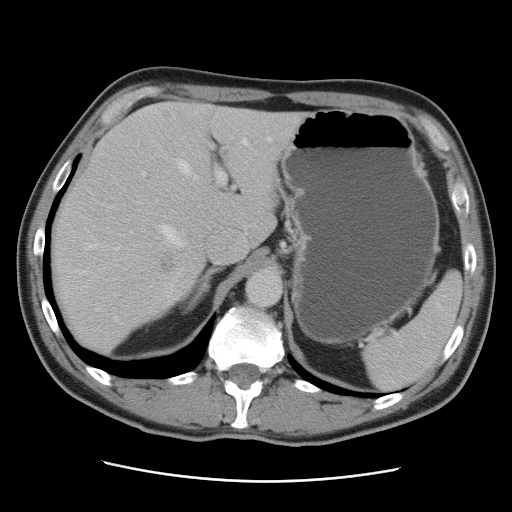
Contrast-enhanced abdominal CT, one axial slice; intravenous contrast given; soft-tissue window (W 400 / L 40 HU); 5 mm slice thickness; 512 × 512 image matrix, field of view 366 × 366 mm. Male patient, age 59 years. From the clinical record (not read from this slice): diagnosis: colorectal cancer liver metastases, imaged before liver resection; multiple liver metastases: yes; largest metastasis: 0.6 cm; chemotherapy before resection: no.
Outlined on this slice (outlined manually by an expert reader):
- hepatic veins: bounding box <75,138,271,274> (left, top, right, bottom; pixels)
- liver: <50,103,308,352>
- planned liver remnant (the part of the liver to remain after resection): <93,102,292,246>
- portal vein (with intrahepatic branches): <131,170,226,233>
- liver metastasis: <164,265,175,273>